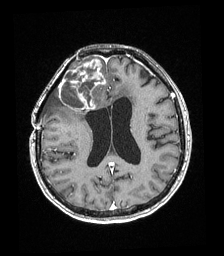
Brain MRI from a brain-tumour surgery series, one axial slice. Position 84 of 192 along the scan axis. T1-weighted post-contrast. 224 × 256 image matrix, field of view 219 × 250 mm. Case-level facts recorded for this patient, not image findings: histopathology: Astrocytoma; WHO grade: 4; IDH mutation: yes; tumour location: Right superficial frontal.
Outlined on this slice (expert manual segmentation):
- tumour: bounding box (x1, y1, x2, y2) in pixels: (59, 60, 105, 110)